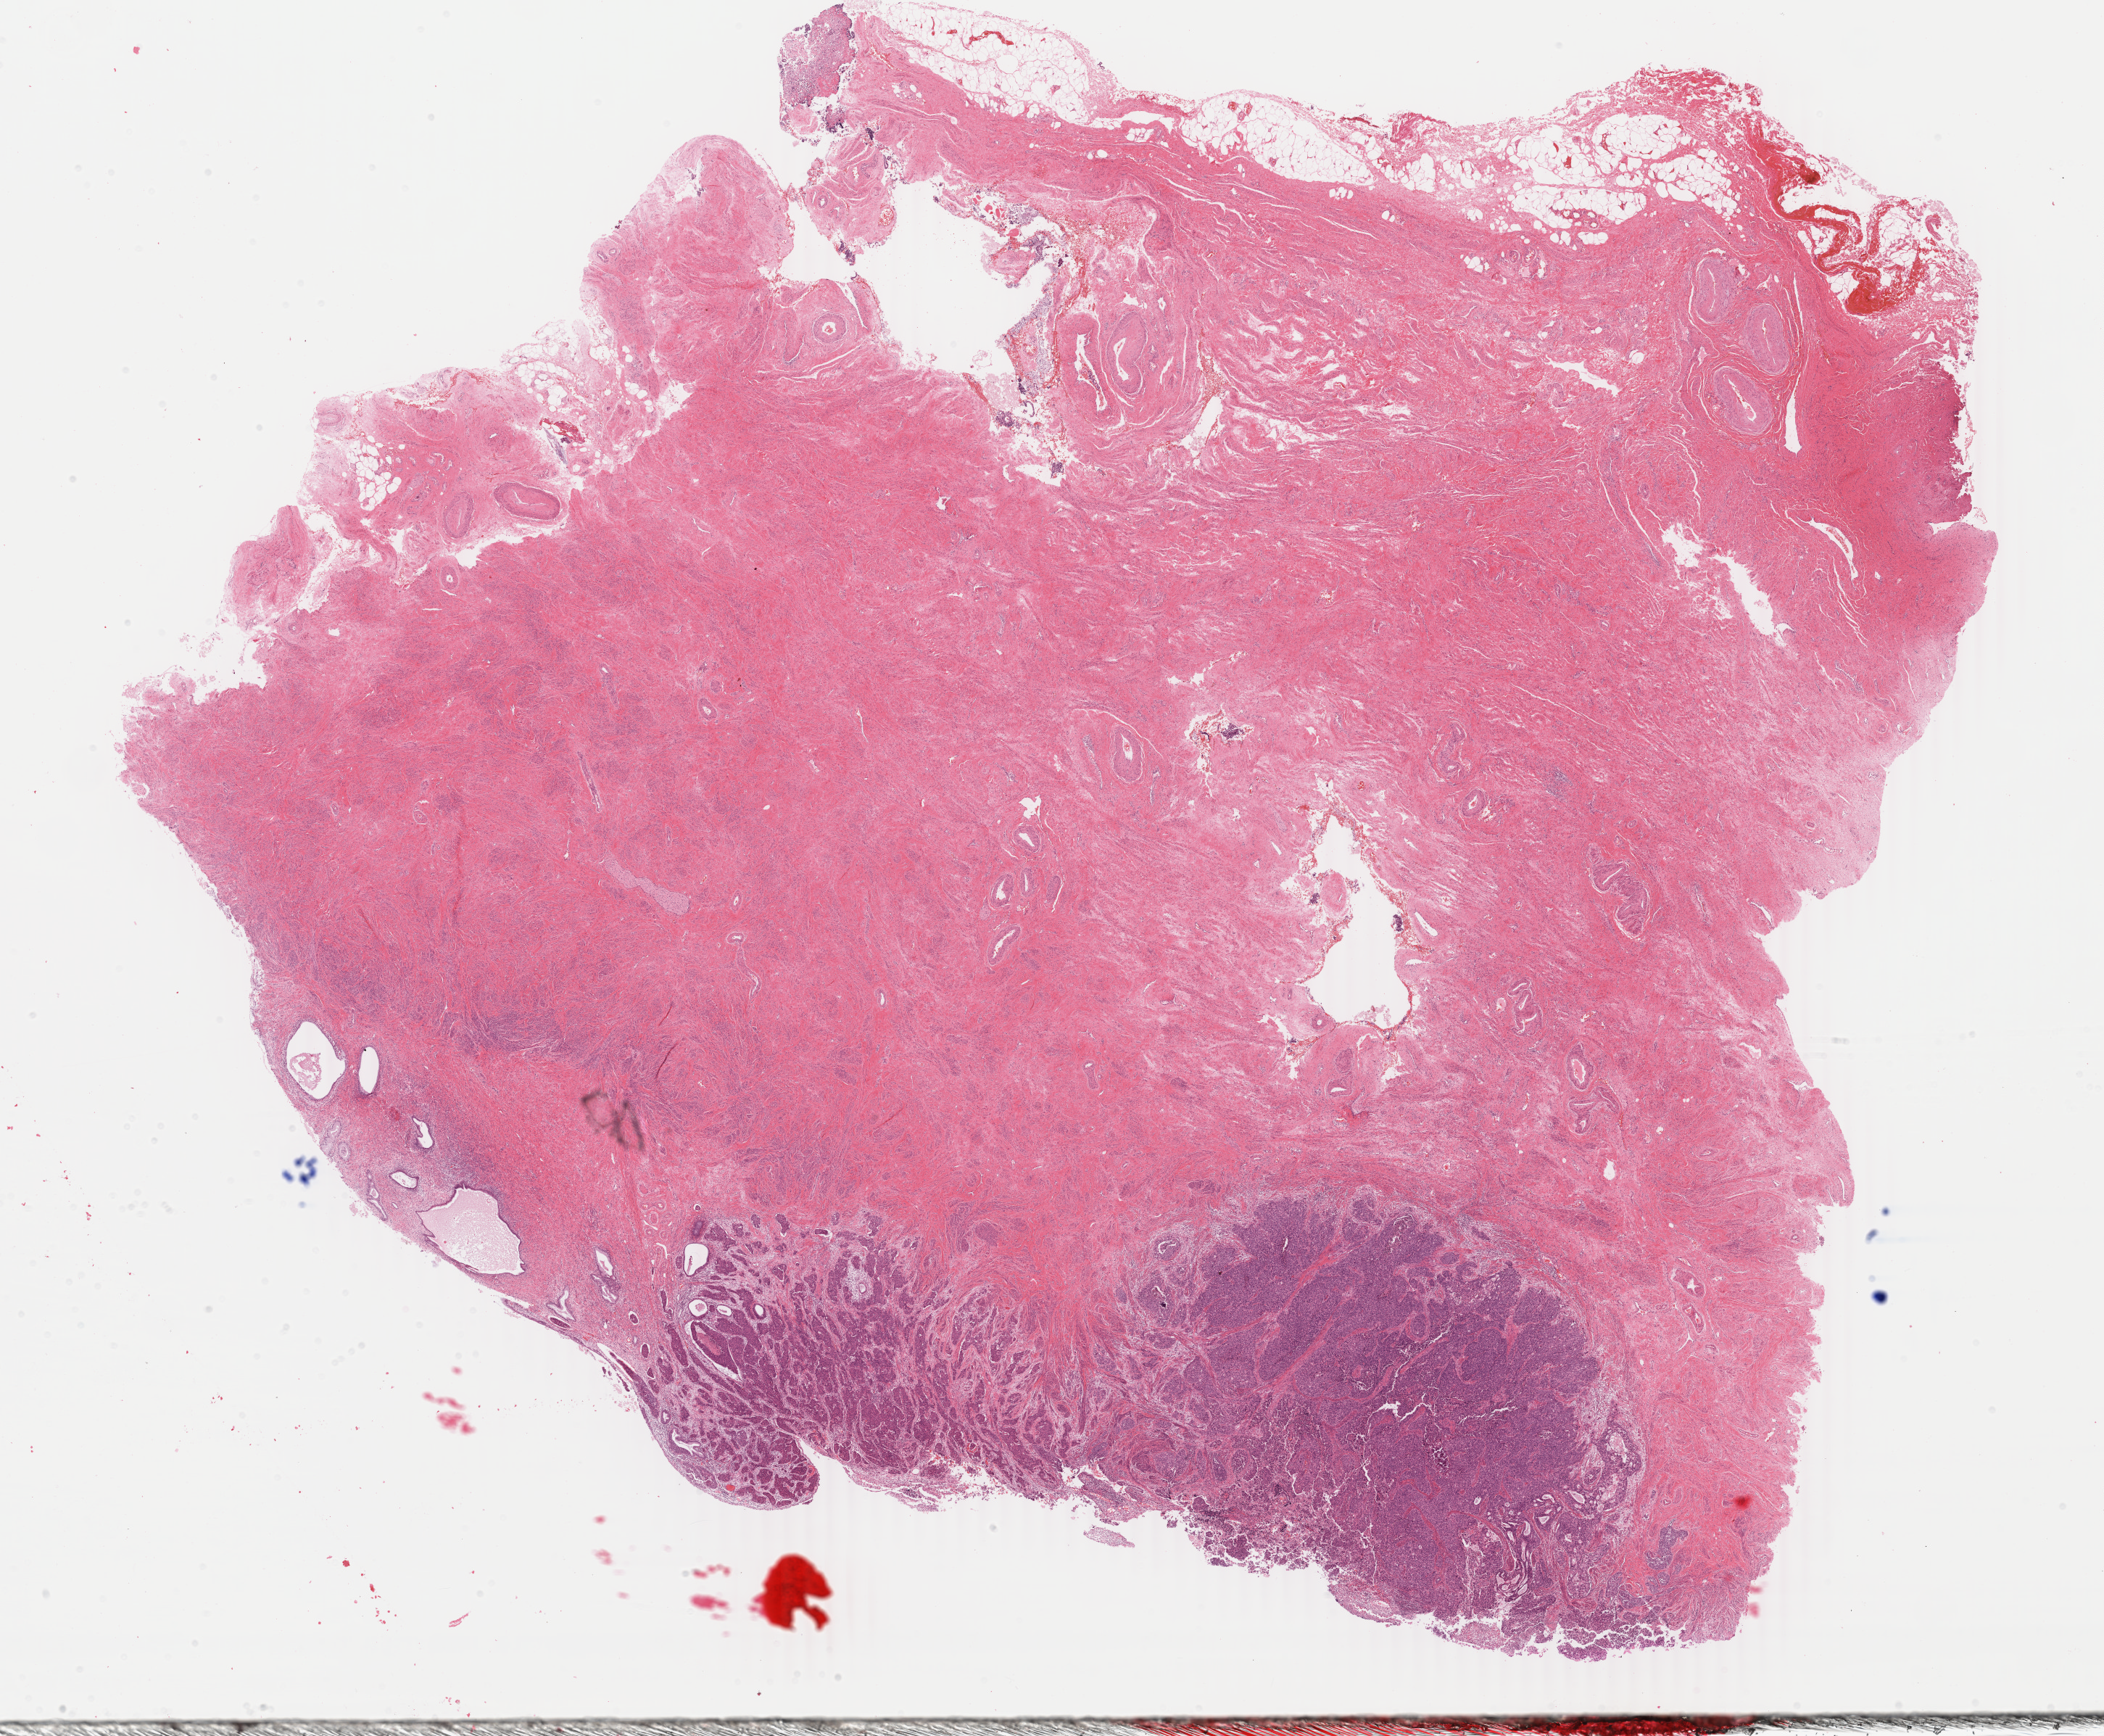
Digitized H&E-stained tissue section (whole slide), shown as a low-resolution overview of the whole scanned area (about 23.1 x 19.0 mm). FFPE section. Sample: primary tumour, cervix. Patient: female, age at initial diagnosis 56 years. Histologic grade: G2 (moderately differentiated).
* FIGO stage: IB1
* pathologic diagnosis: Squamous cell carcinoma, NOS (cervix uteri)